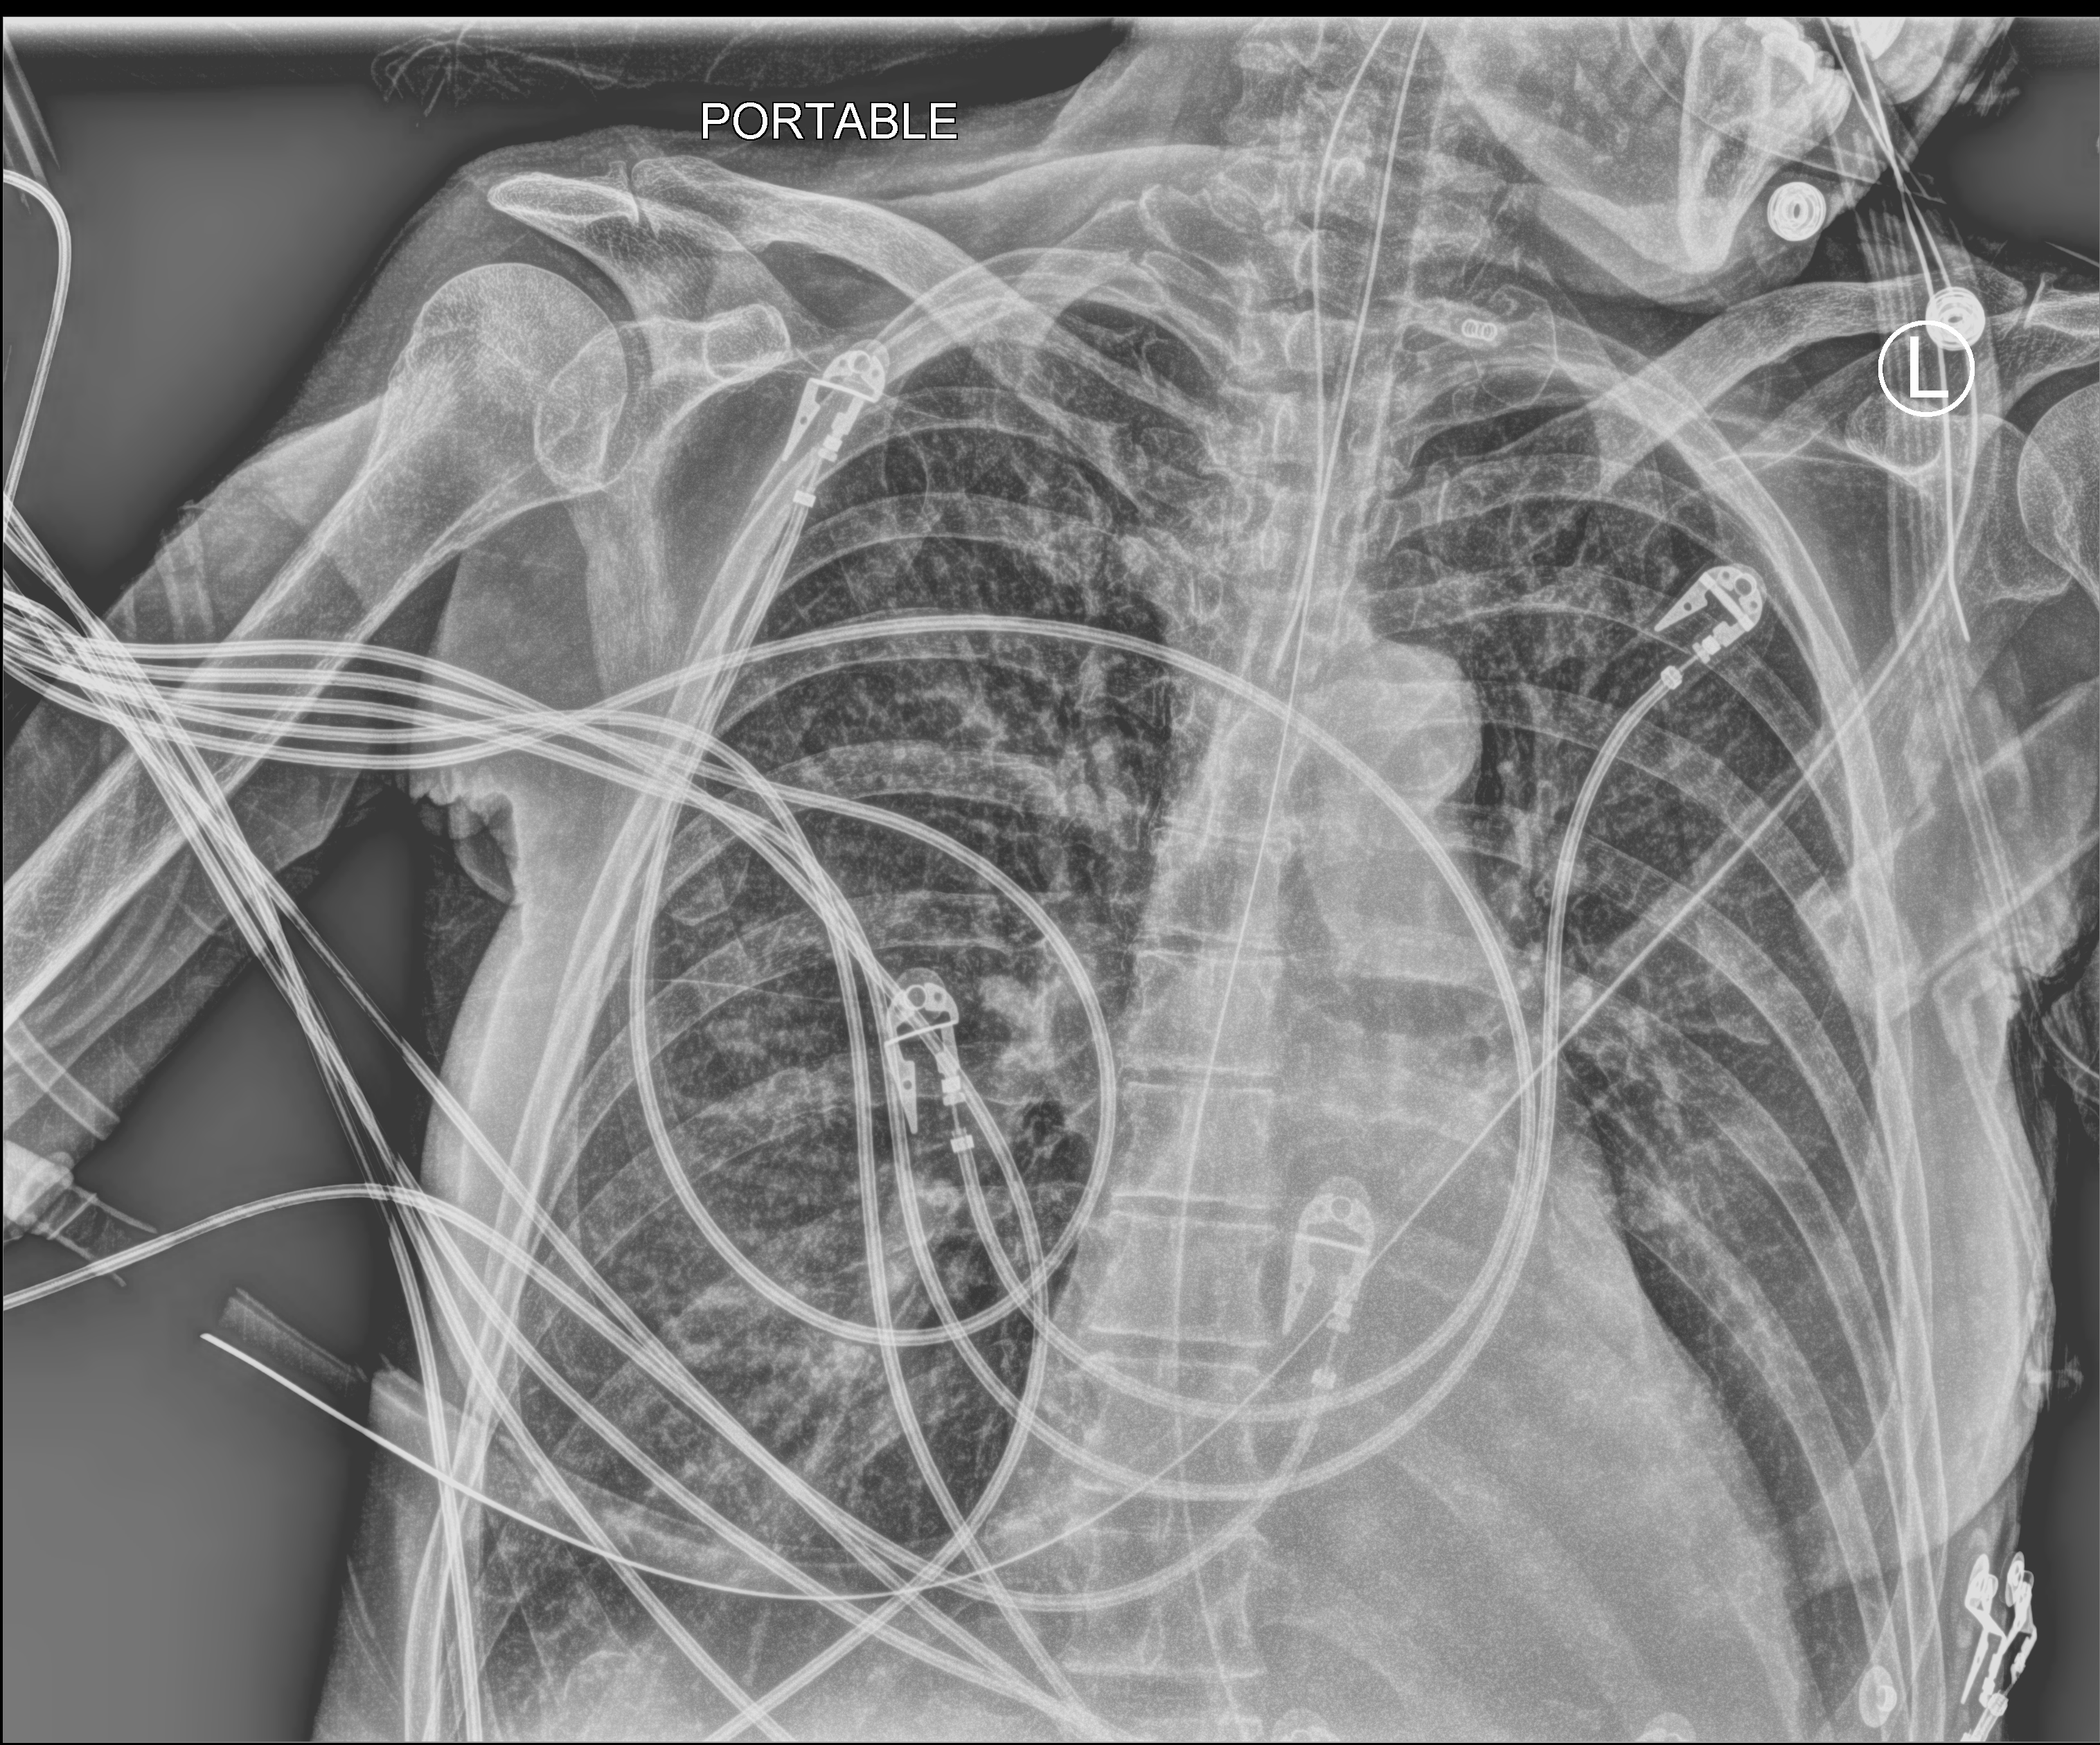
Portable chest radiograph, anteroposterior (AP) projection. Female patient hospitalised with COVID-19, age 60–74 years.
From the hospital-stay record, not from the radiograph (when in the stay this image was taken is not recorded):
- mechanically ventilated during this hospital stay: yes